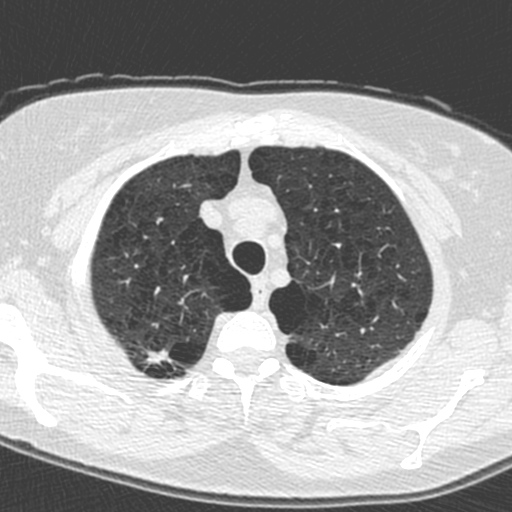
Chest CT (low-dose screening protocol), one axial image. Baseline annual screen. Lung window (W 1500 / L -600 HU). 1.3 mm slice thickness. Standard (soft-tissue) reconstruction kernel (C). 120 kVp. Slice 22 of 224 in the series. 512 × 512 image matrix. Female participant, aged 59 years at enrolment. Current smoker at enrolment.
Expert reader's lesion annotation, bounding box (x1, y1, x2, y2) in pixels: (132, 335, 177, 376). No non-calcified nodule or mass ≥4 mm was recorded by the screening reader at this exam. Official screen result: negative screen, minor abnormalities not suspicious for lung cancer. Later outcome: lung cancer diagnosed 881 days after this screen — adenocarcinoma, NOS, right upper lobe, poorly differentiated (G3), stage IA (AJCC 6th edition), 20 mm at pathology.